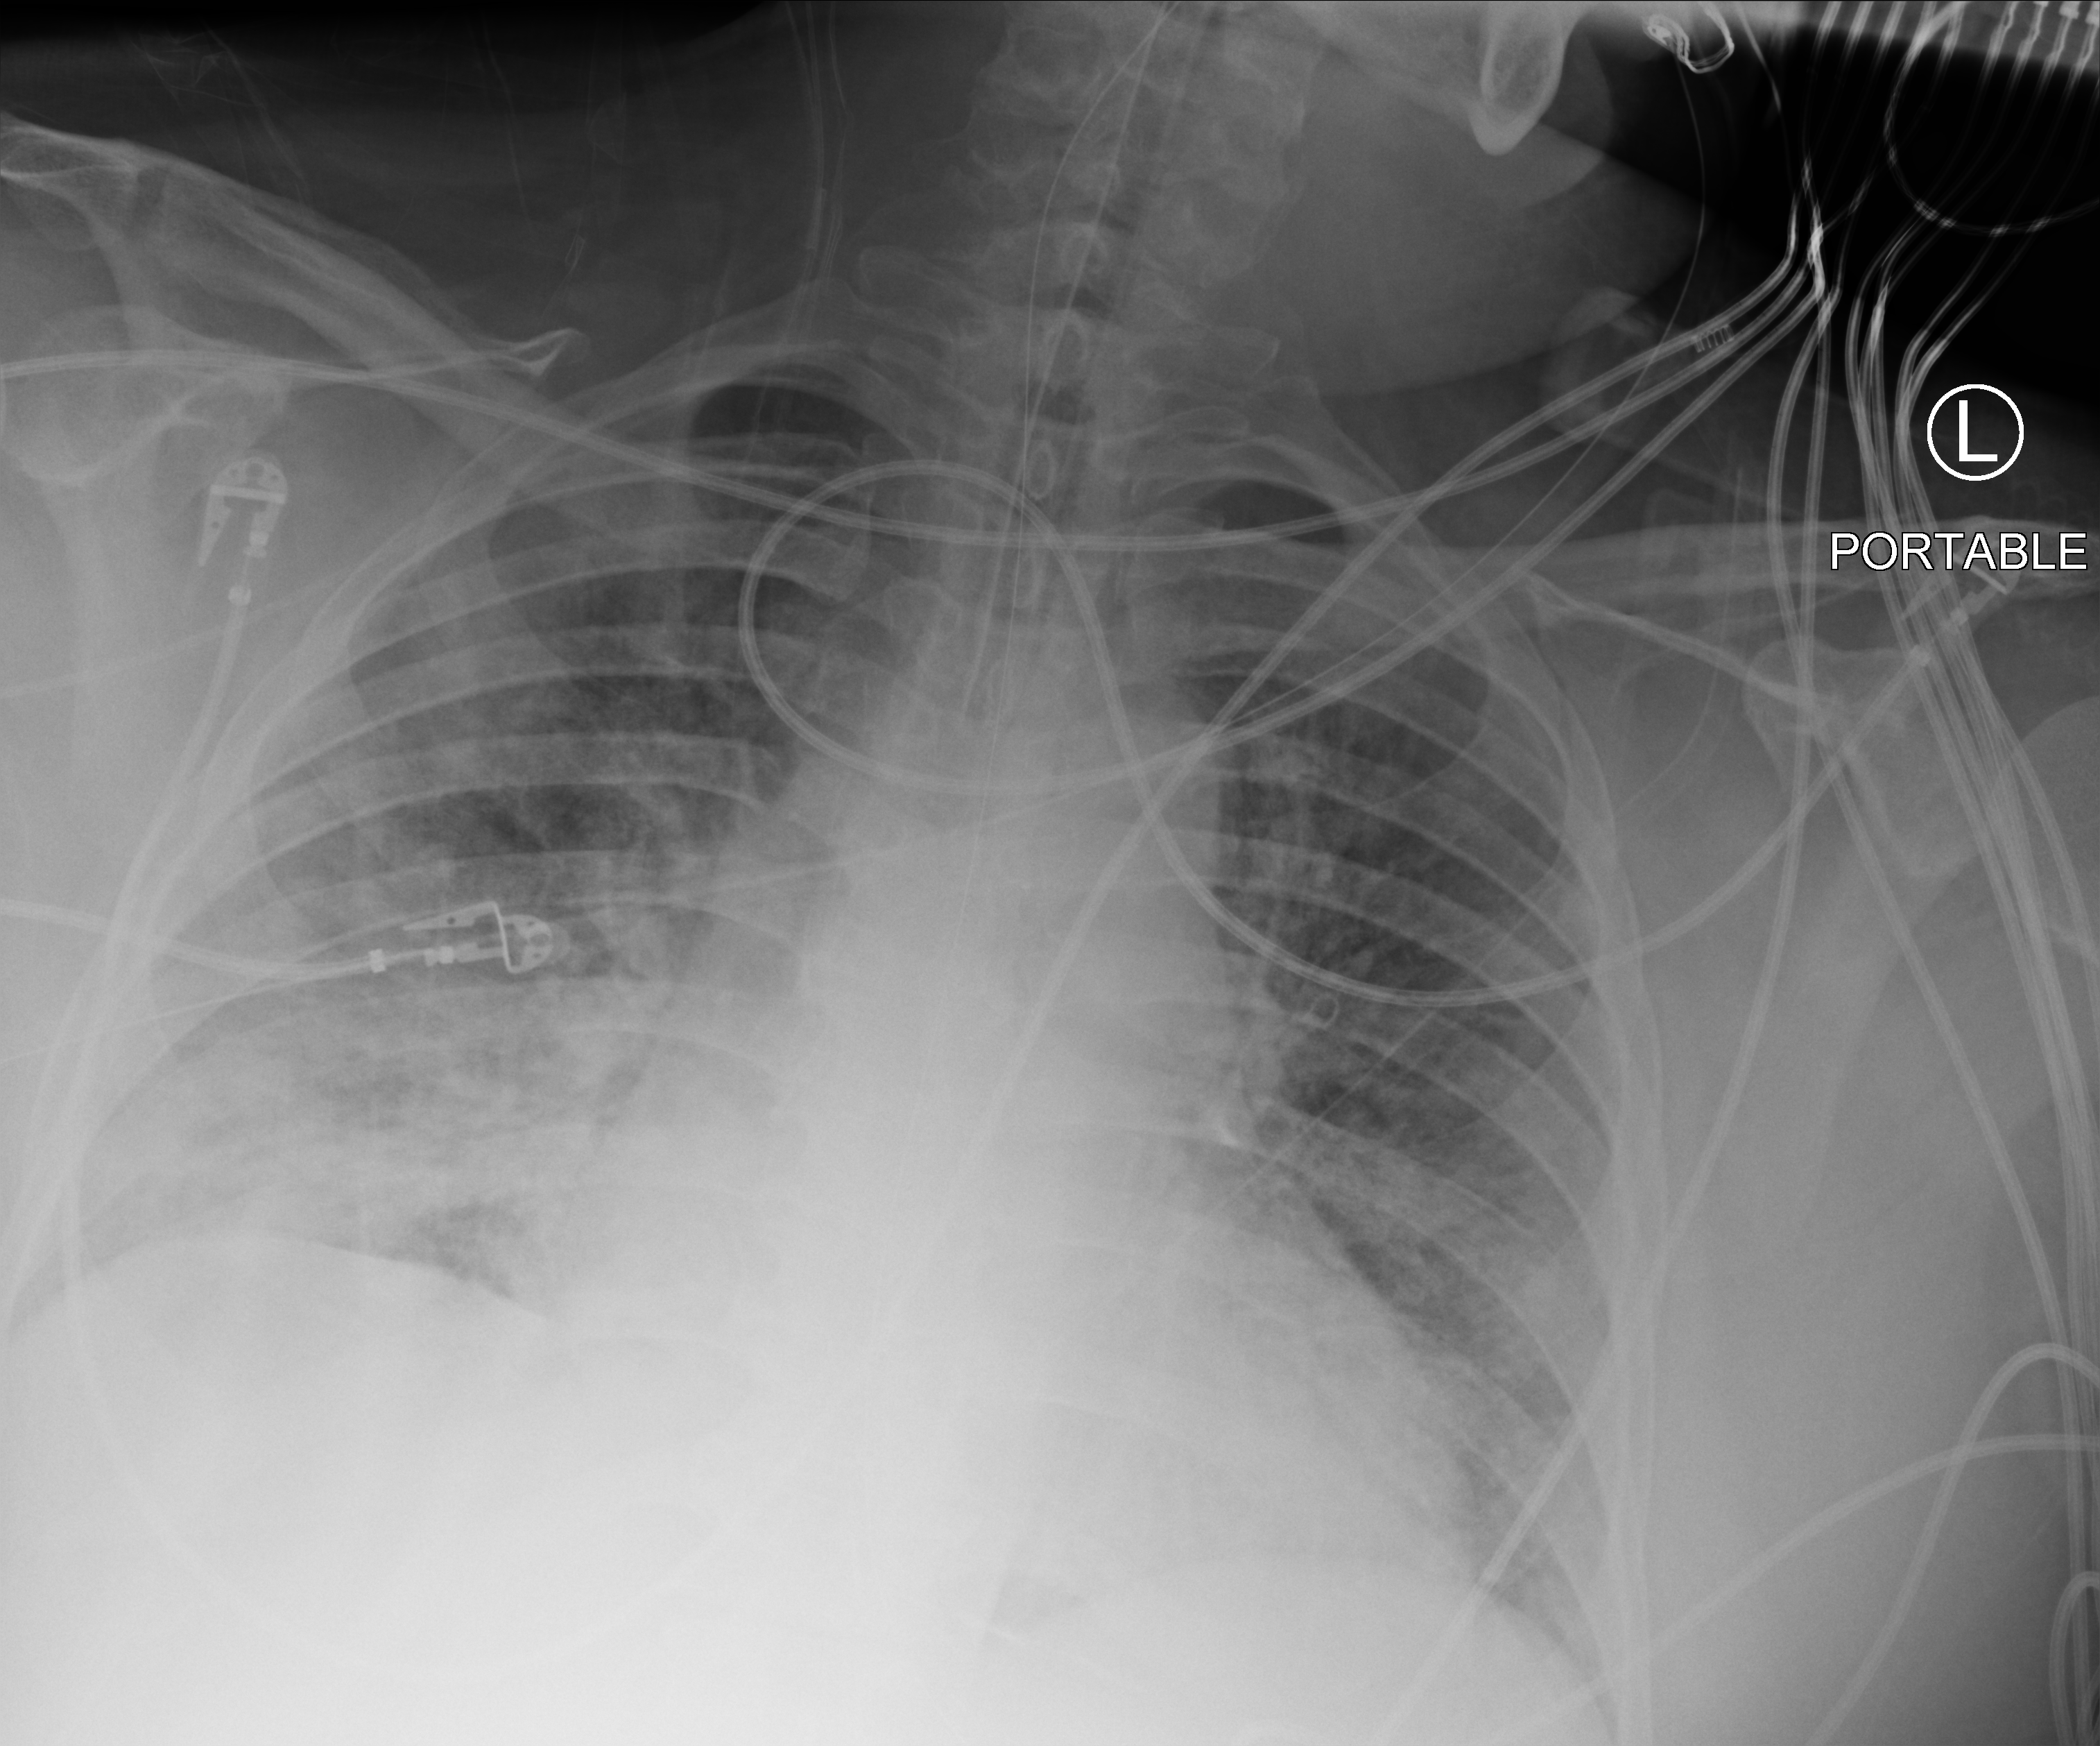
Portable chest radiograph; anteroposterior (AP) projection. Patient hospitalised with COVID-19; male, aged 18–59 years.
From the hospital-stay record, not from the radiograph (when in the stay this image was taken is not recorded): admitted to intensive care during this hospital stay: yes; mechanically ventilated during this hospital stay: yes.